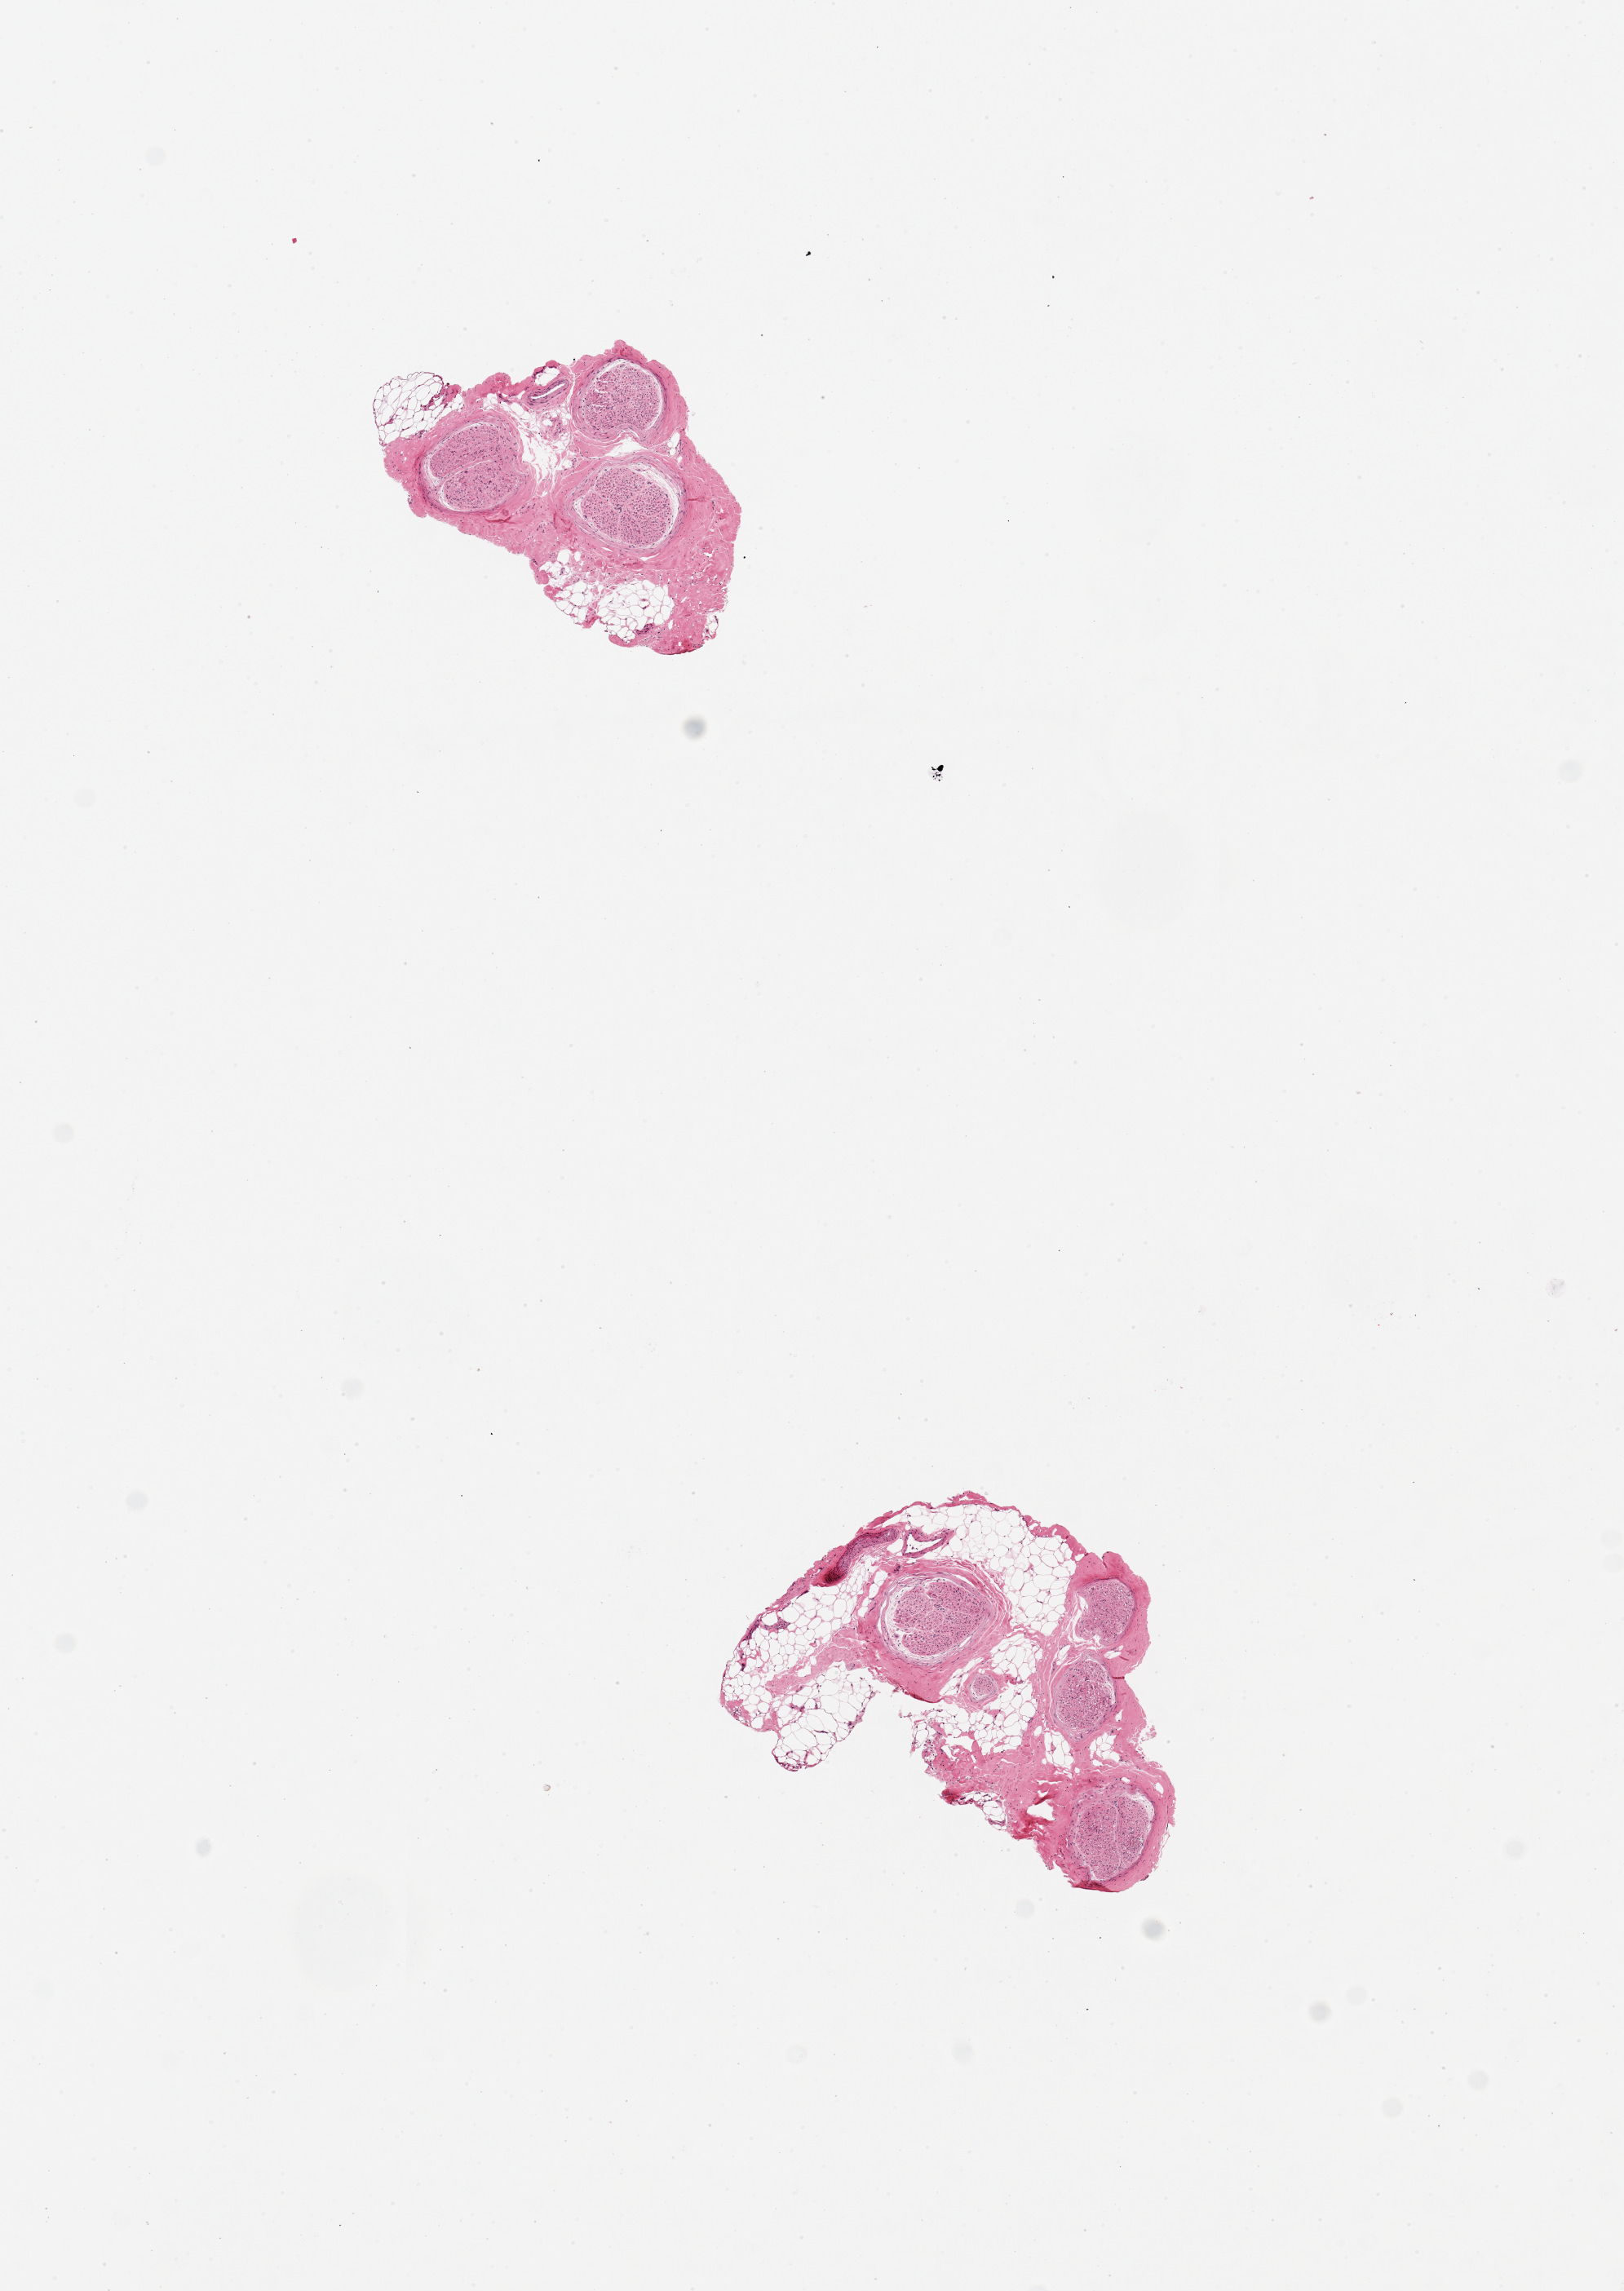
Digitized H&E-stained section — whole scanned area (about 7.9 x 11.1 mm, acquisition: 20x scan) shown as a low-resolution overview, PAXgene-fixed, paraffin-embedded tissue, sampled site (target tissue): tibial artery, tissue donor sample. Donor: male.
• reviewer comment on this tissue sample: 2 pieces, 2x1 & 2x2mm; peripheral nerve: unknown origin